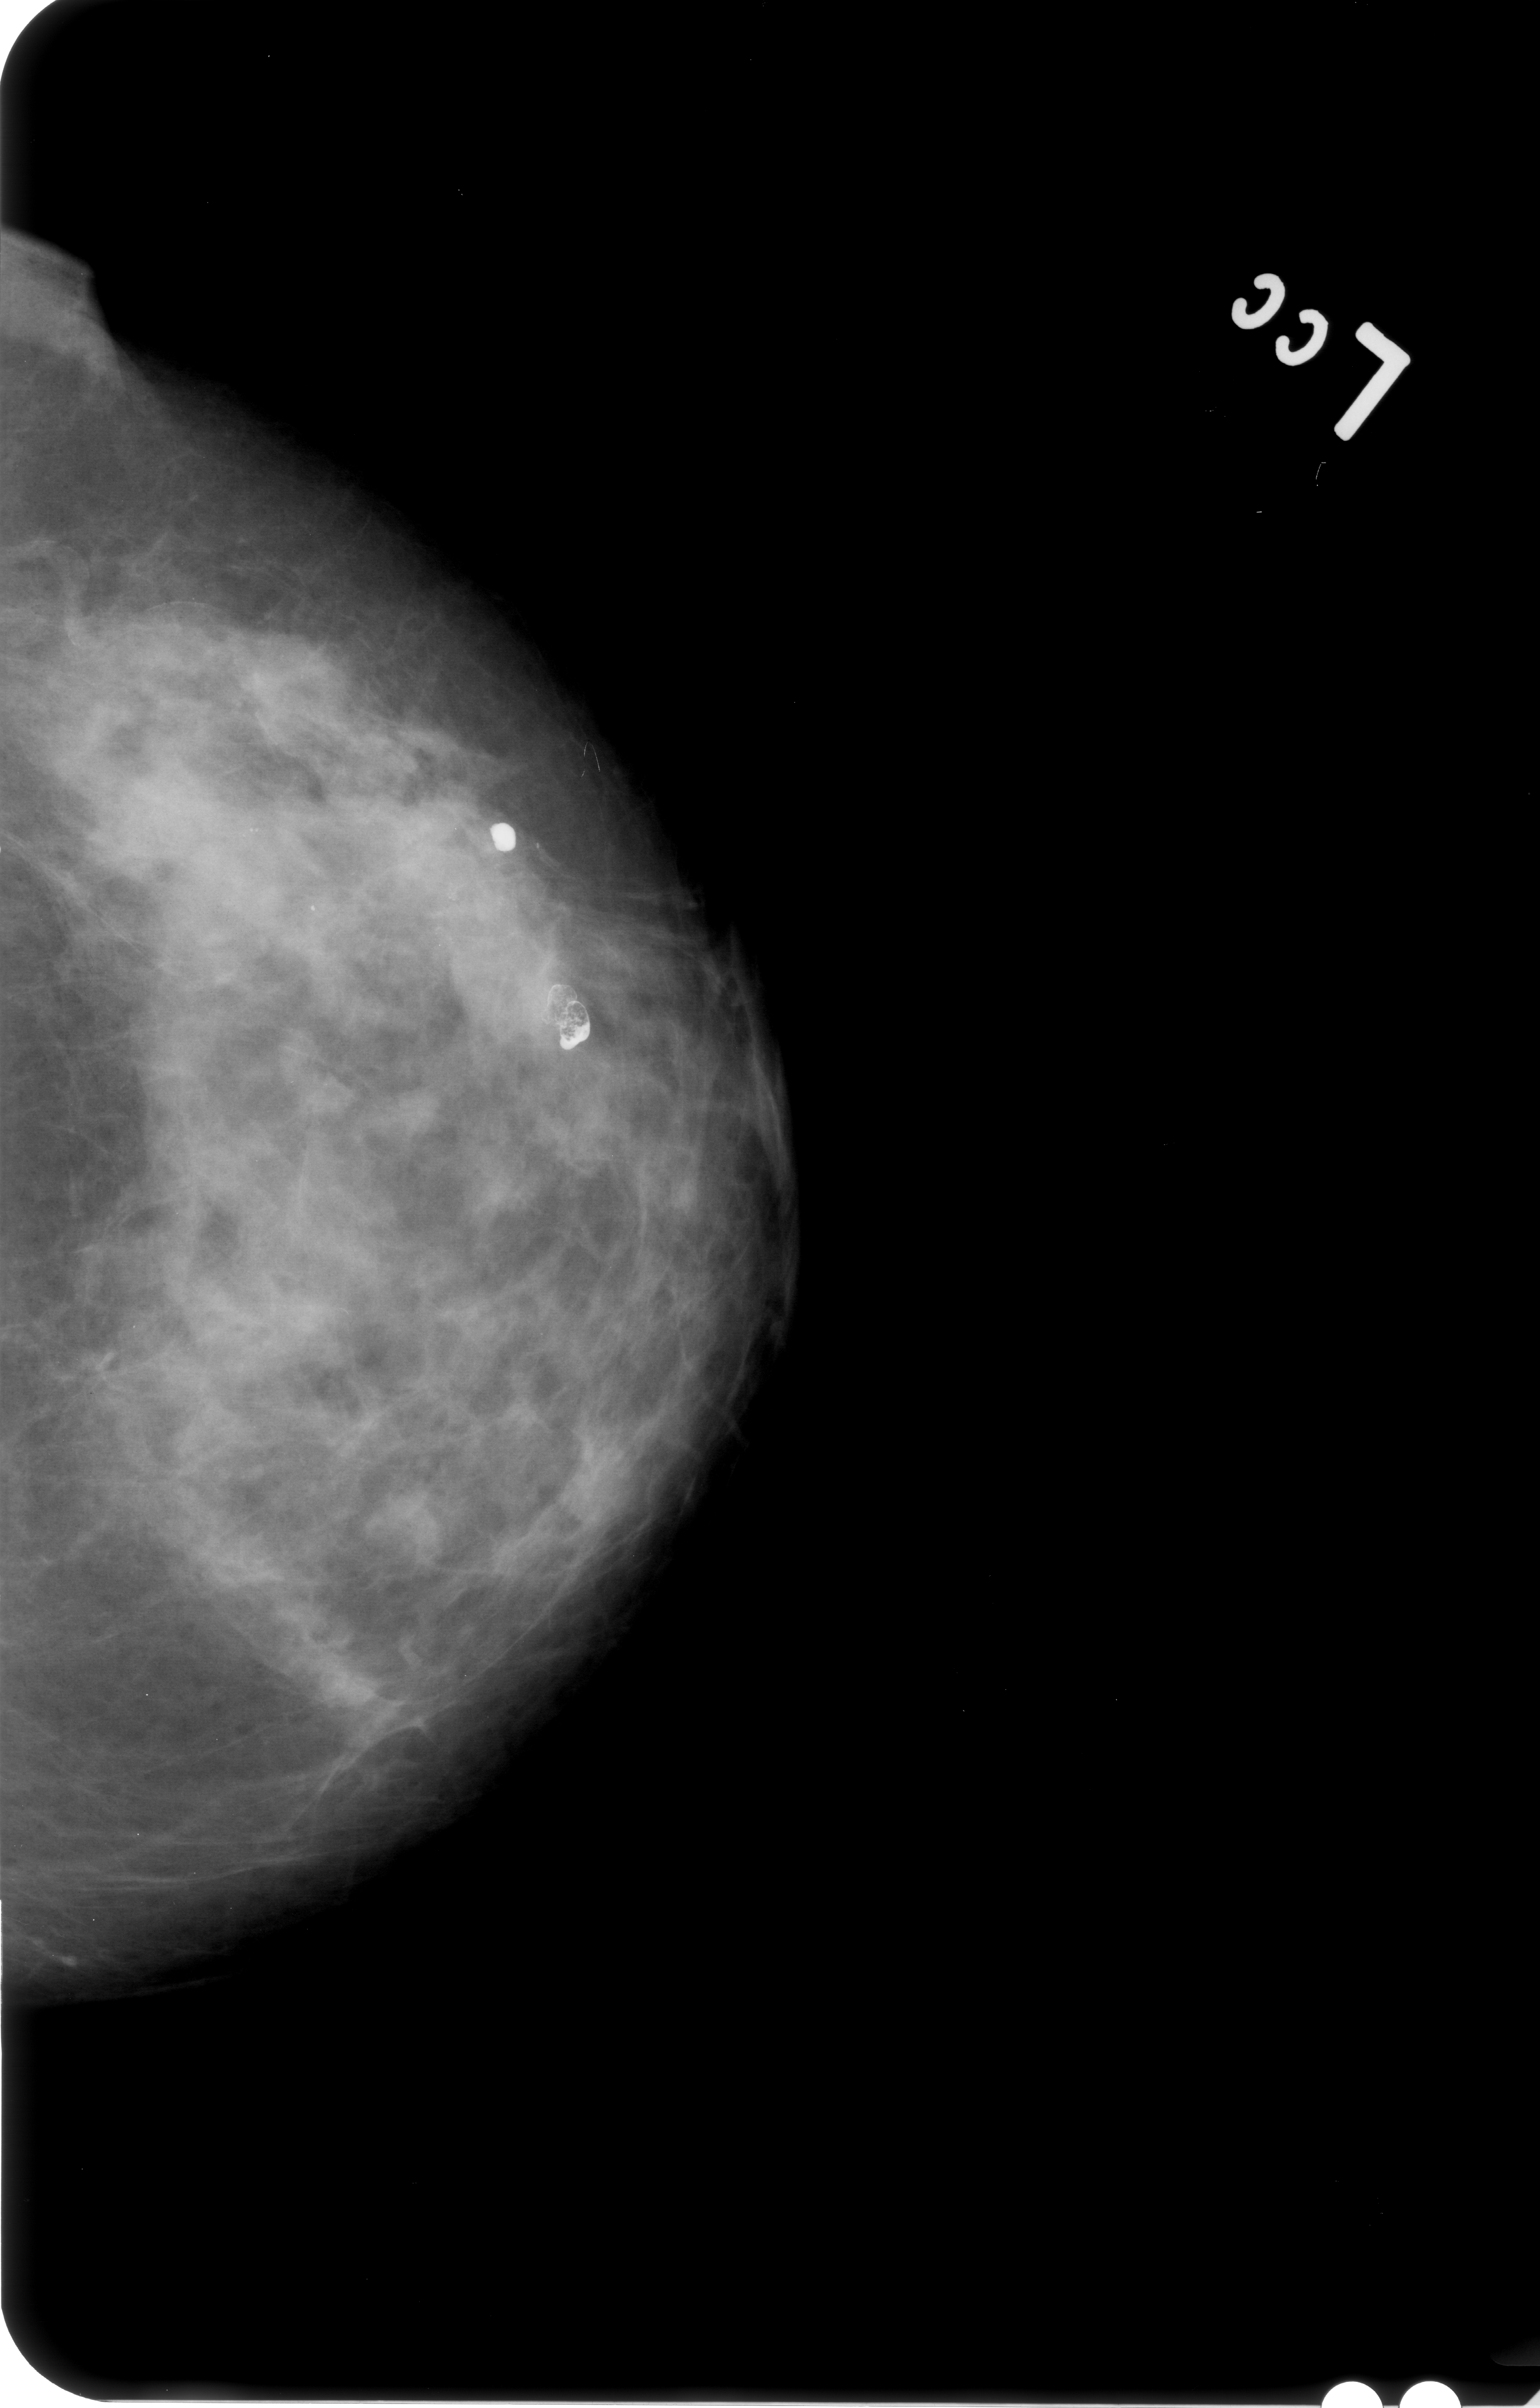
Mammogram (digitized film), left breast, CC view, BI-RADS breast density category 3 (scale 1–4).
Marked findings (only marked abnormalities are described; nothing is implied about the rest of the image): calcifications, morphology punctate, distribution segmental; BI-RADS assessment category 4; subtlety rating 2 on a 1 (subtle) to 5 (obvious) scale; pathology (as recorded): malignant.